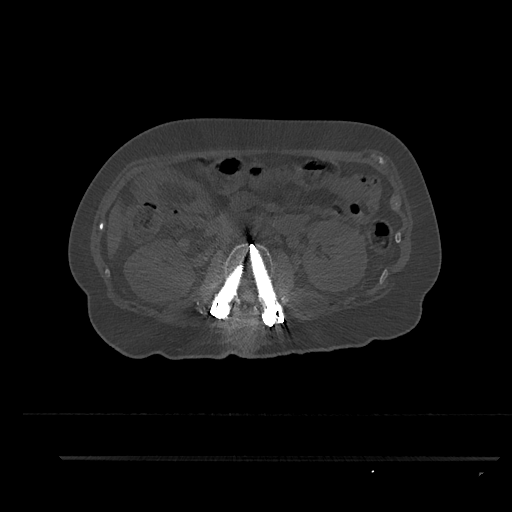
CT including the spine, one axial slice; slice 168 of 797 in the series (ordered by position); reconstruction kernel Br40s/3; 120 kVp; bone window (W 1800 / L 400 HU); 512 × 512 image matrix, field of view 408 × 408 mm. Patient: female, 44 years. From the clinical record (not read from this slice): primary cancer: renal.
Outlined on this slice (semi-automatic segmentation, software-assisted and operator-edited):
- L2 vertebra: bounding box <207,243,284,320> (left, top, right, bottom; pixels)